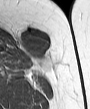
MRI of an extremity soft-tissue mass, one axial slice; position 23 of 45 along the scan axis; MR volume resampled by the dataset authors to the PET/CT grid (not the native acquisition matrix); 3.27 mm slice thickness; 90 × 109 image matrix. Female patient. Case-level facts recorded for this patient, not image findings: histological type: leiomyosarcoma; grade: intermediate; site of the primary tumour: parascapusular.
Structures marked on this image (expert contour drawn on MRI and transferred to this co-registered scan by the dataset authors):
- gross tumour volume including surrounding oedema: bounding box <17,28,52,67> (left, top, right, bottom; pixels)
- gross tumour volume (mass): <21,28,50,60>